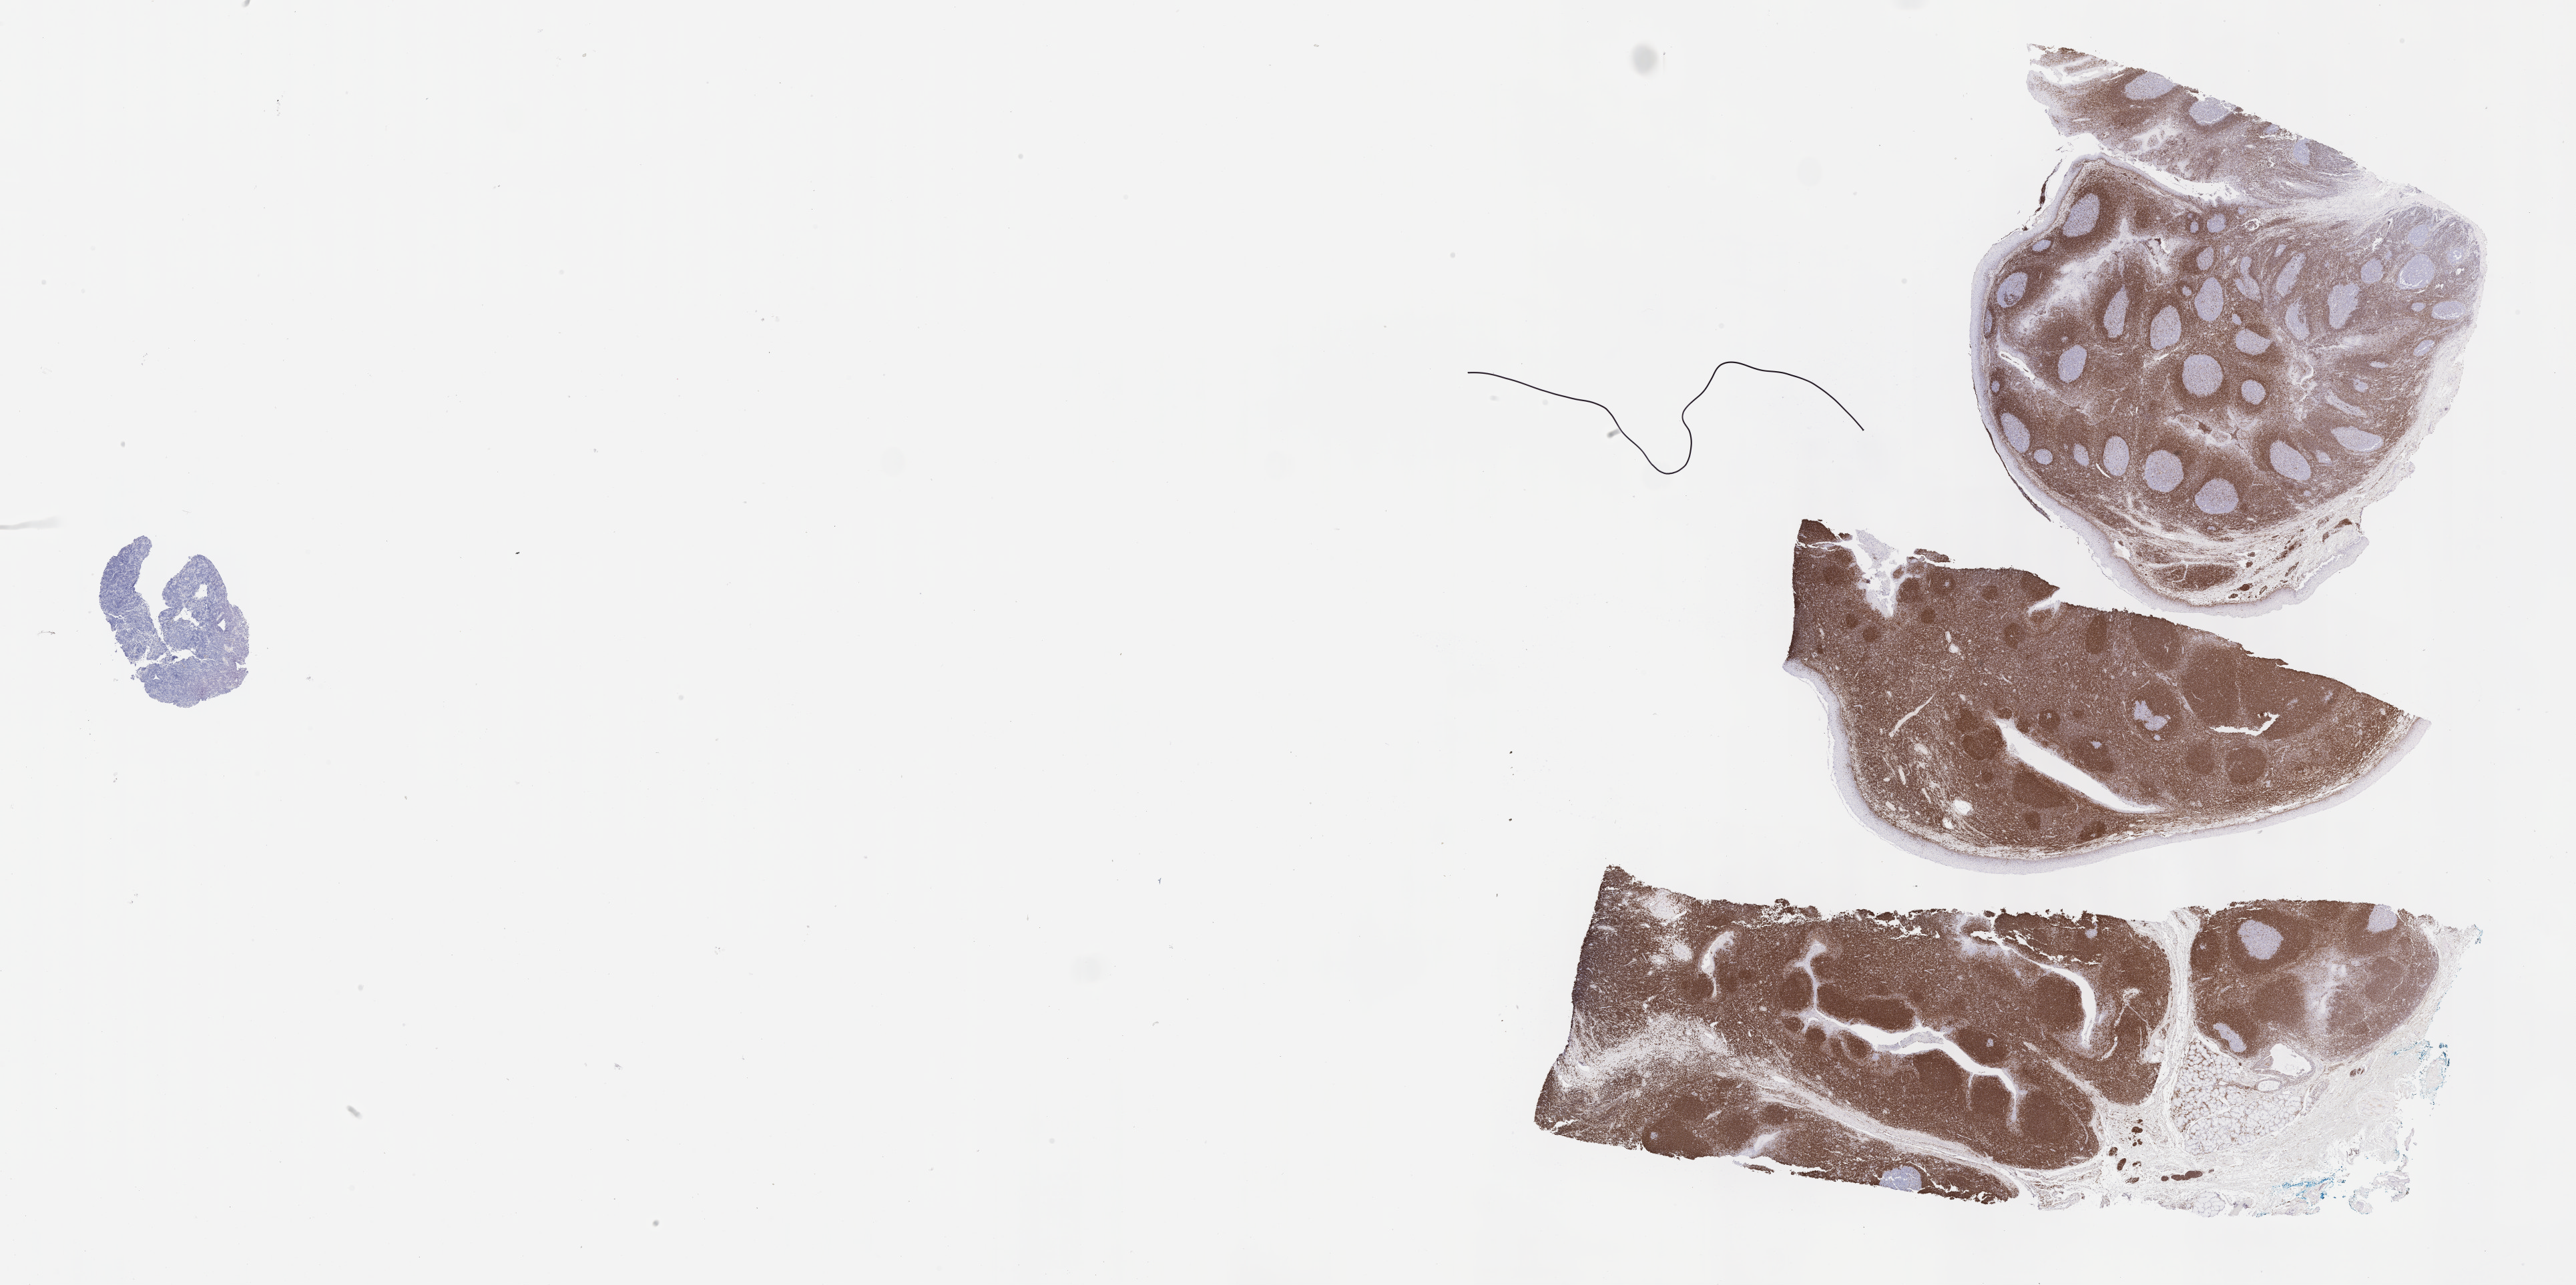
IHC for BCL2, whole-slide image, low-resolution overview of the scanned area, about 31.2 x 15.6 mm; tumor tissue. Female patient; age at initial diagnosis 8 years.
Diagnosis: Burkitt lymphoma, NOS.